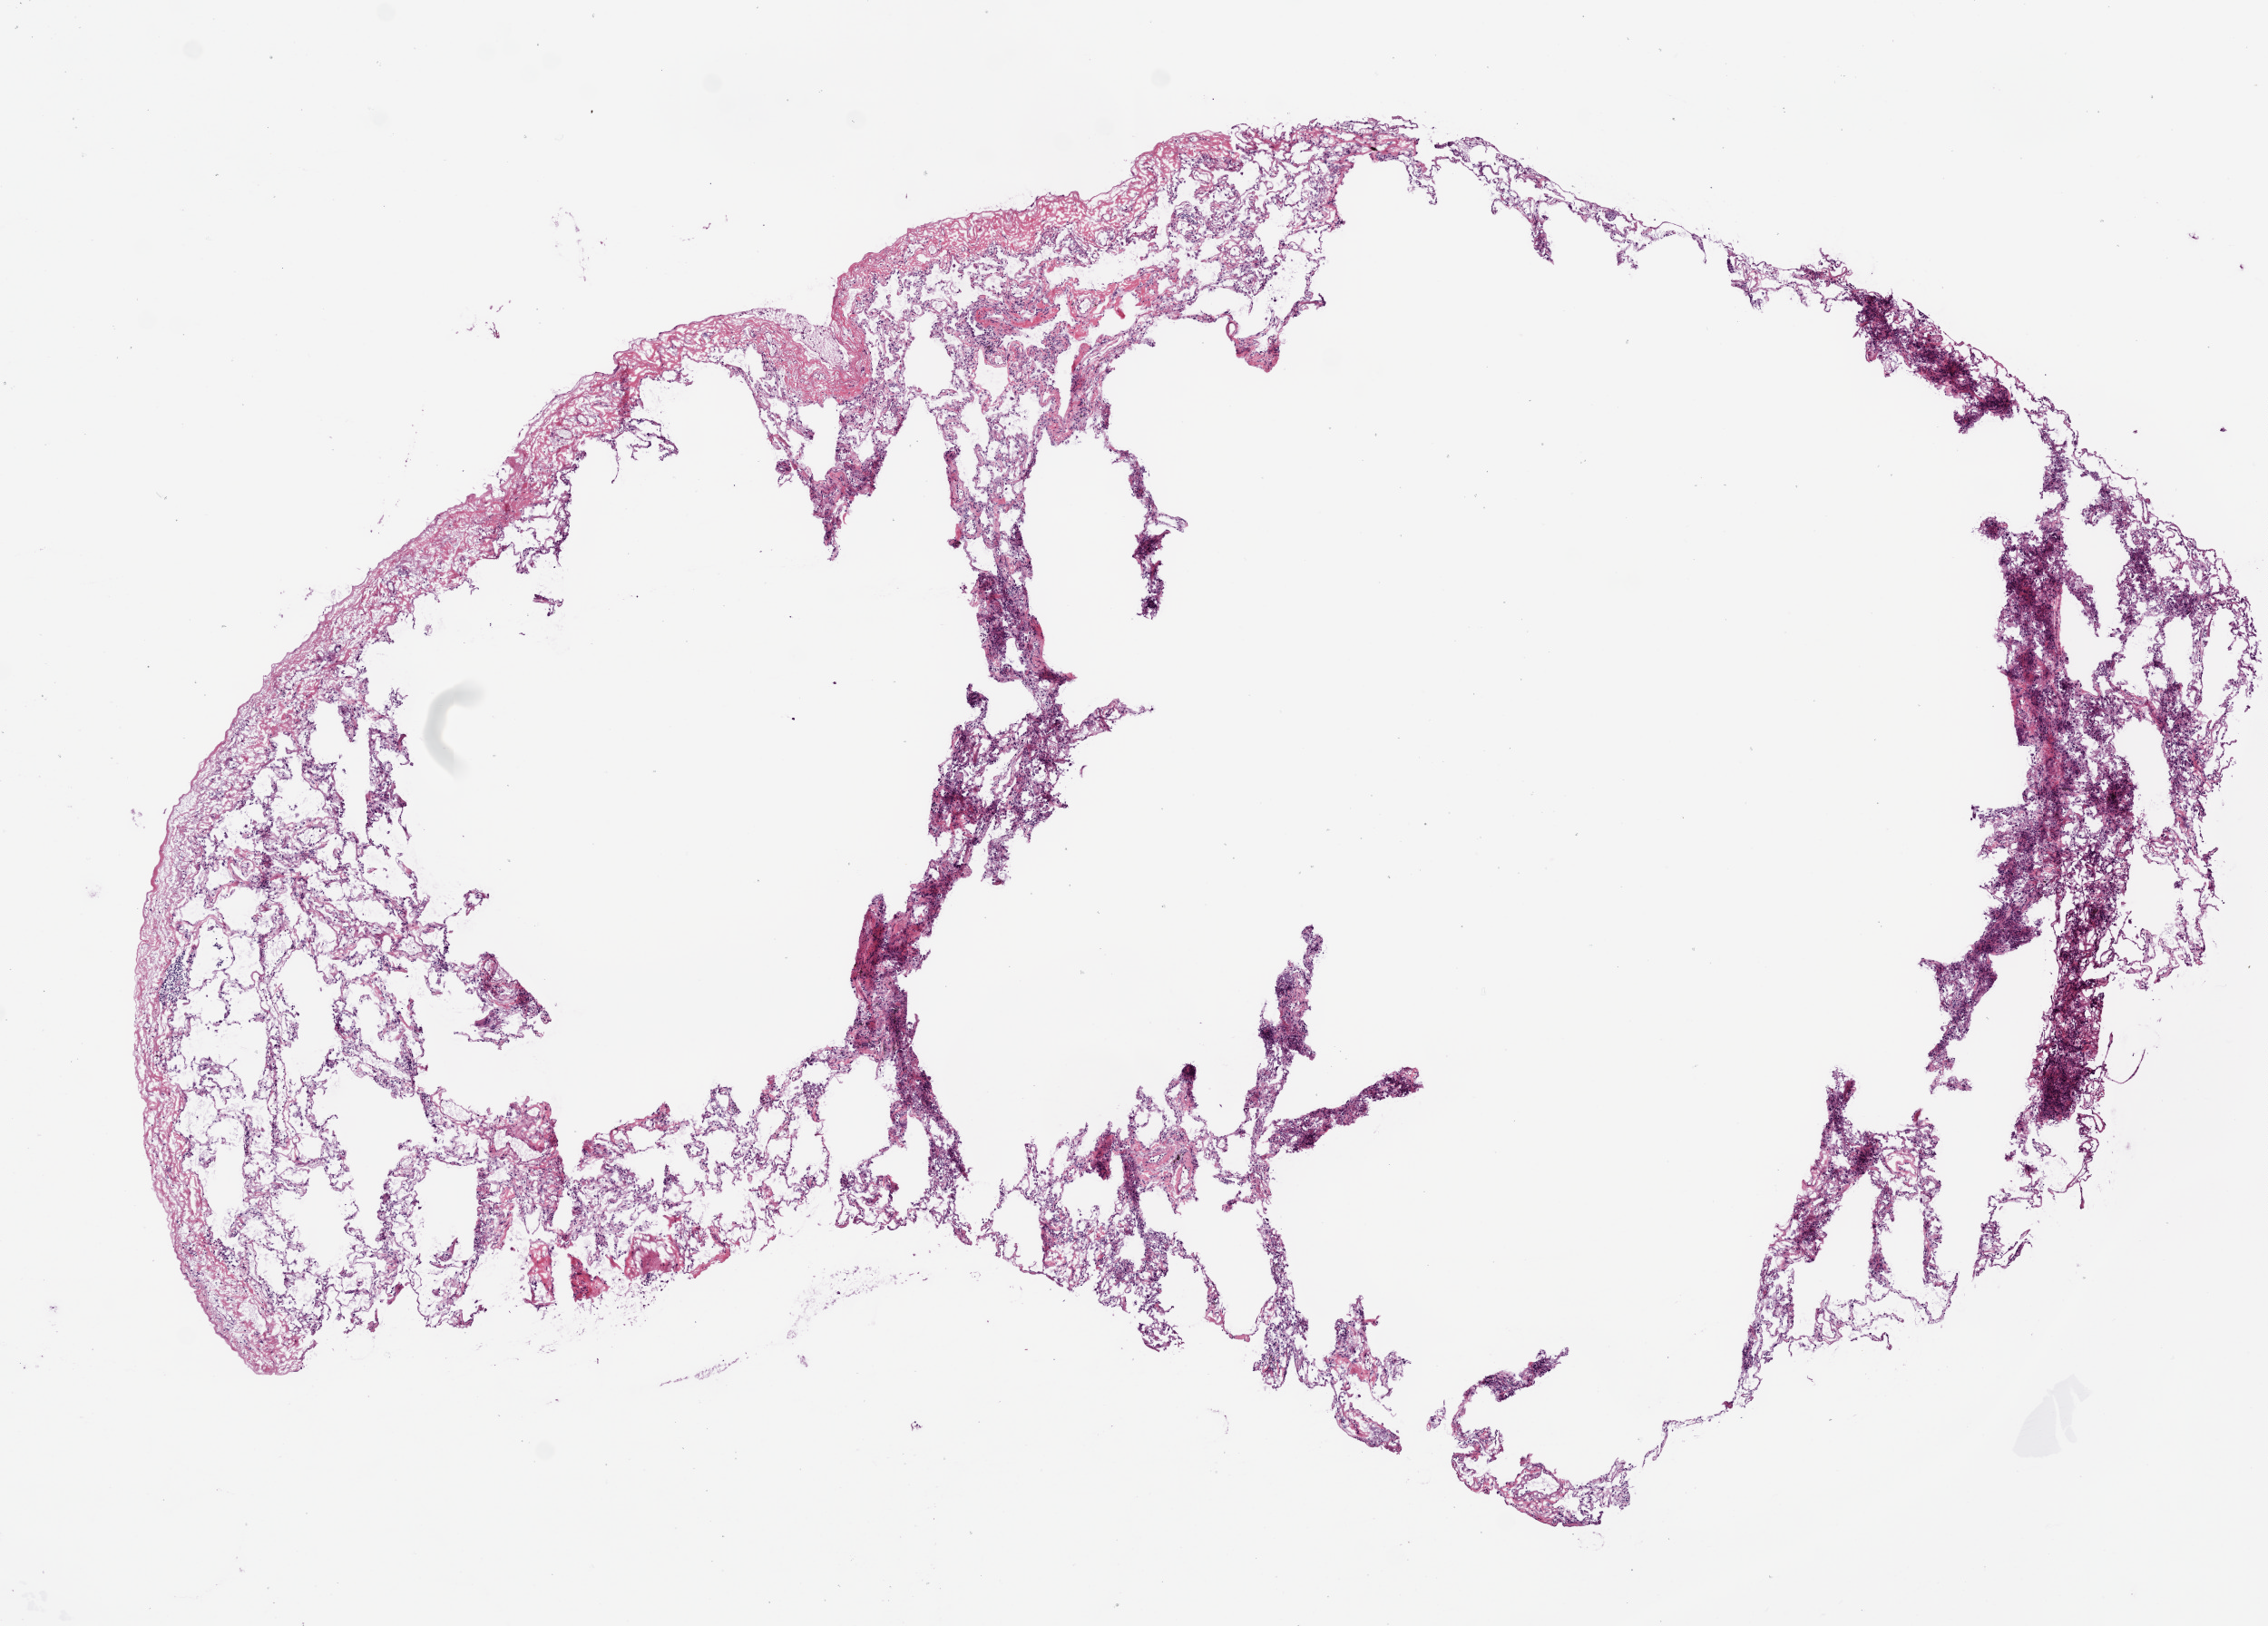
Whole-slide histology image, H&E-stained, a low-resolution overview of the entire scanned area, about 10.0 x 7.2 mm; frozen section; solid tissue normal (non-tumour tissue) sample from the lung. Male patient; age at initial diagnosis 68 years.
This section: solid tissue normal (non-tumour) sample from the same patient. Patient diagnosis: Adenocarcinoma, NOS (upper lobe, lung).